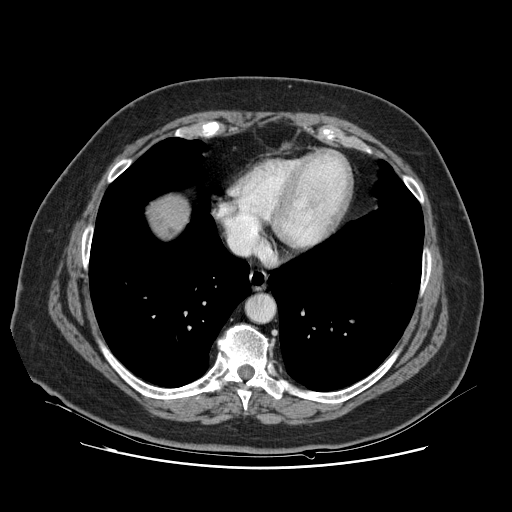
Contrast-enhanced abdominal CT, one axial slice; slice 122 of 132 in the series (ordered by position); intravenous contrast given; soft-tissue window (W 400 / L 40 HU); 2.5 mm slice thickness; 512 × 512 image matrix. Female patient, age 73 years. From the clinical record (not read from this slice): diagnosis: colorectal cancer liver metastases, imaged before liver resection; multiple liver metastases: no.
Outlined on this slice (manually delineated by an expert):
- liver: bounding box (x1, y1, x2, y2) in pixels: (152, 199, 187, 237)
- planned liver remnant (the part of the liver to remain after resection): (152, 199, 187, 237)